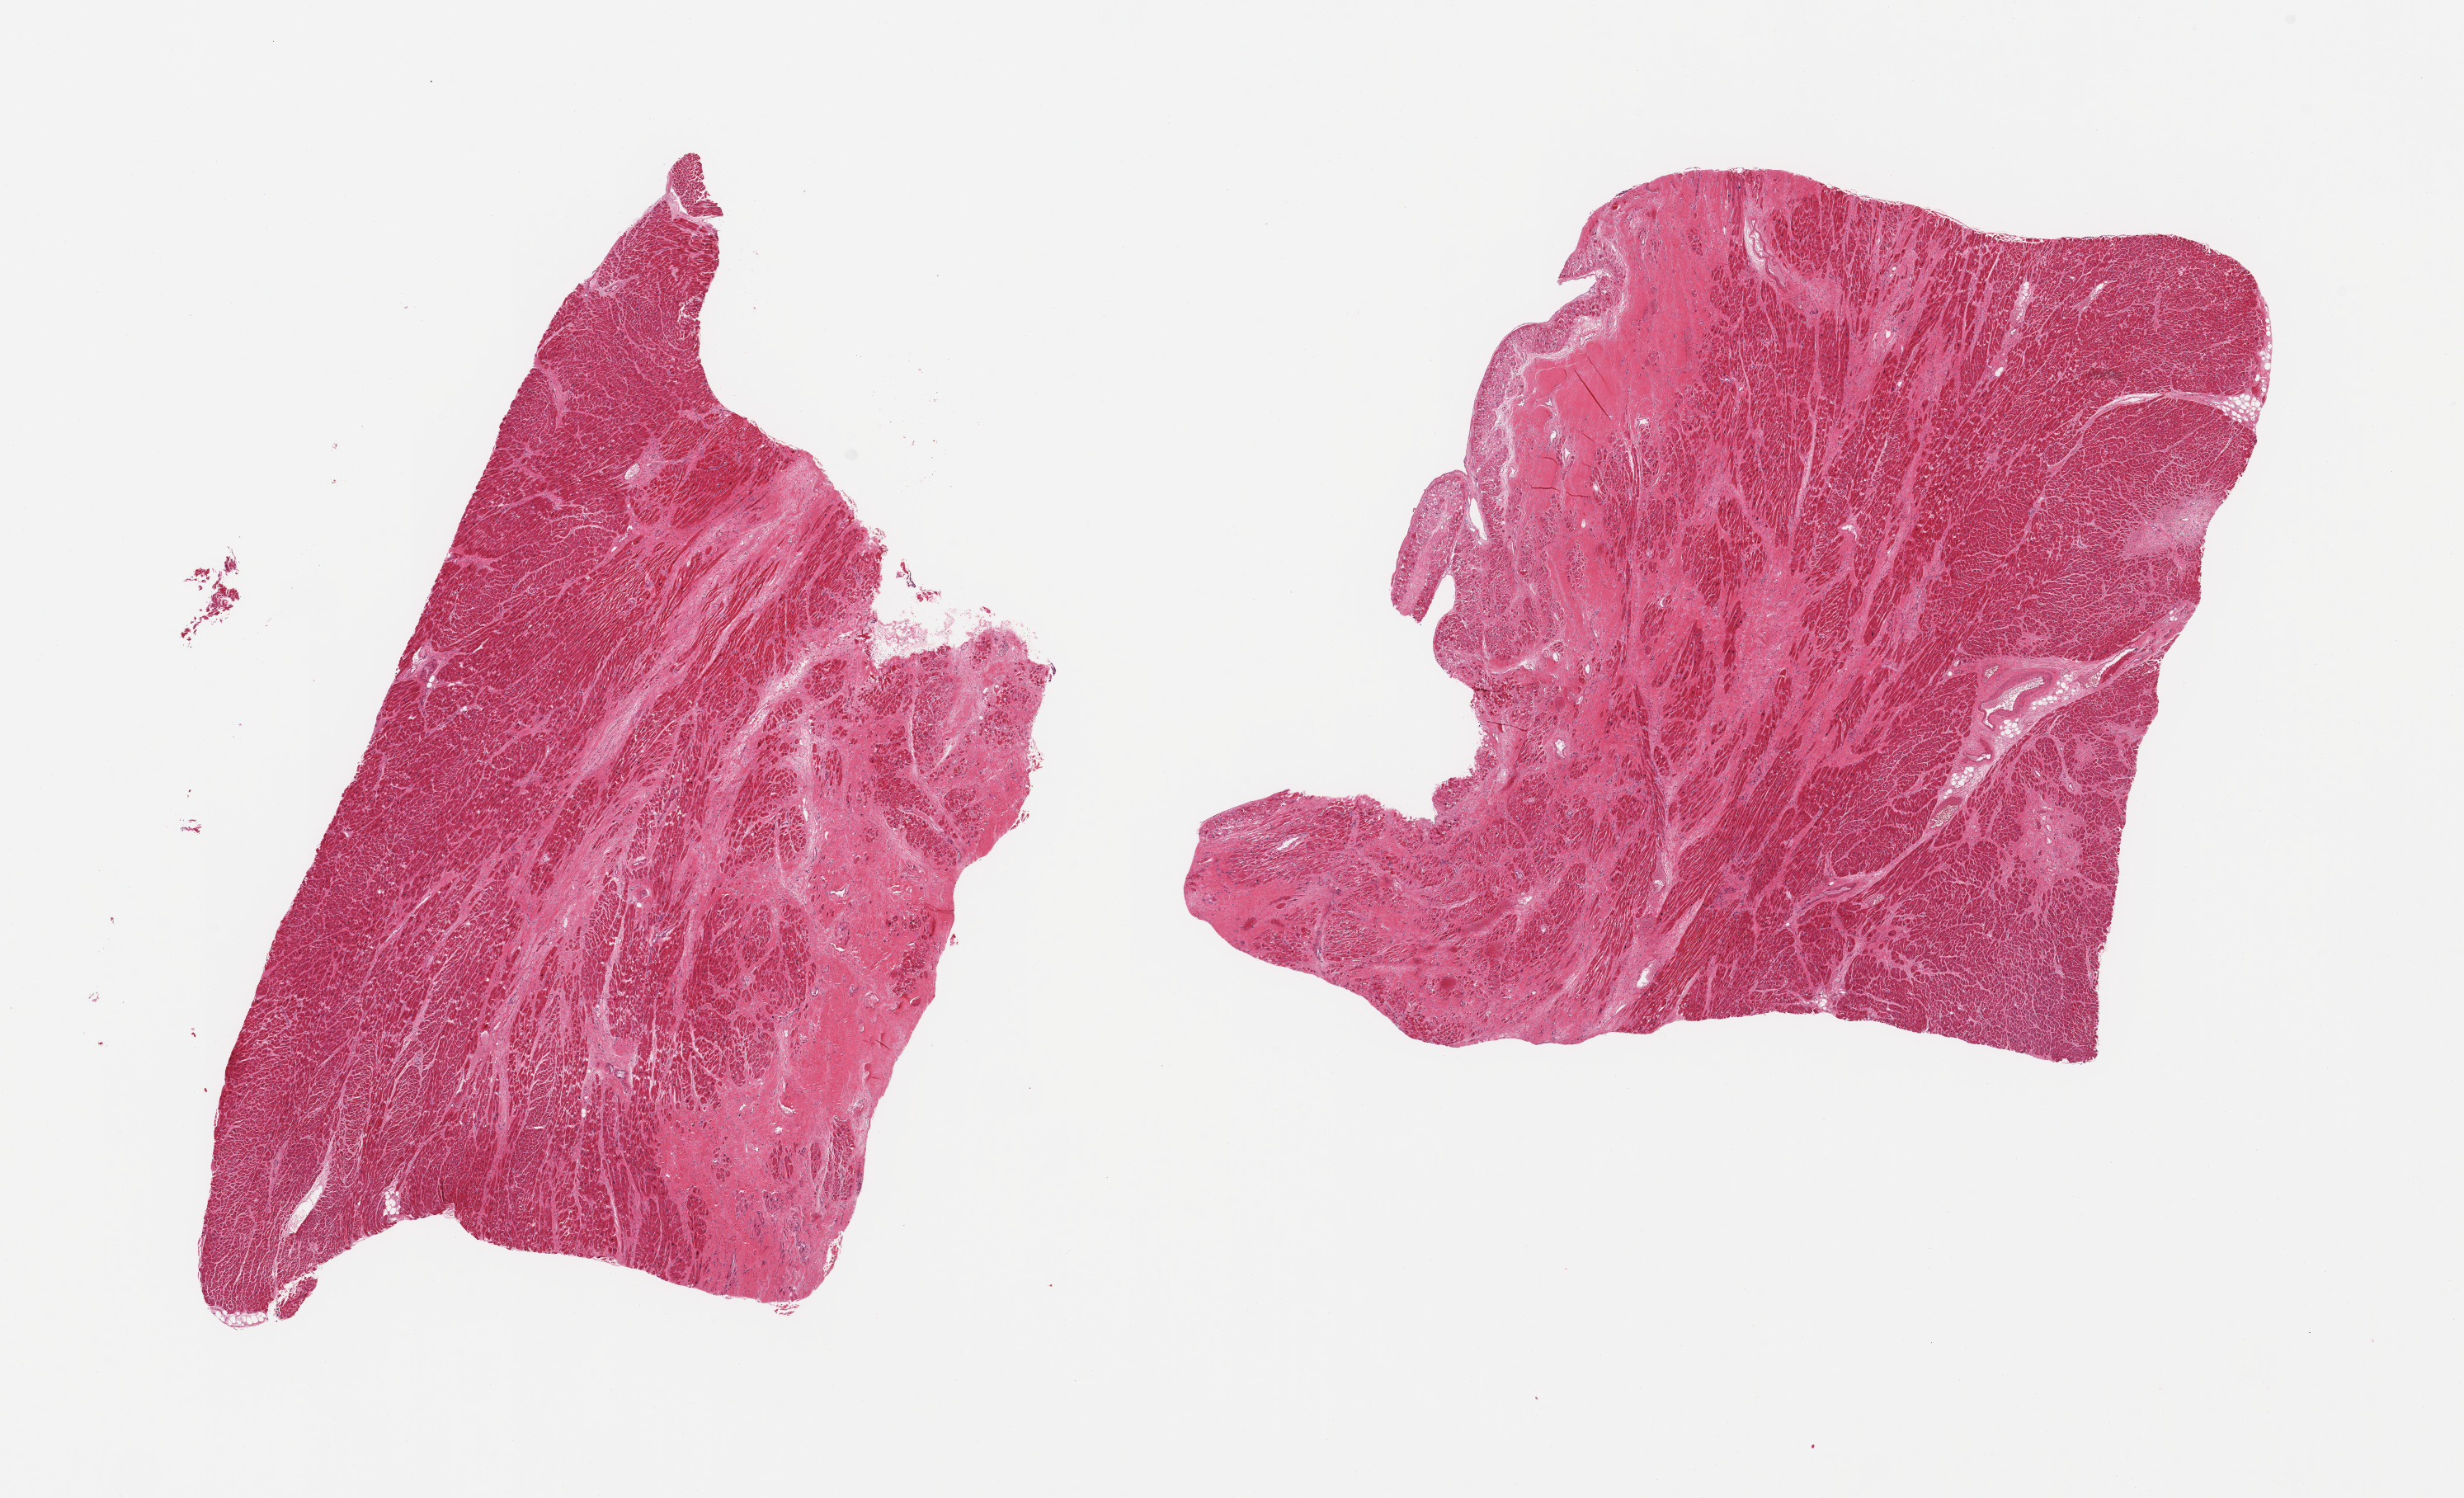
Digitized hematoxylin and eosin (H&E)-stained section — a low-resolution overview of the entire scanned area, about 23.6 x 14.4 mm; PAXgene-fixed paraffin-embedded (PFPE) section; section of heart (target tissue); donor tissue sample.
Reviewer comment on this tissue sample: 2 pieces, remoted infarcts, severe chronic ischemic changes.